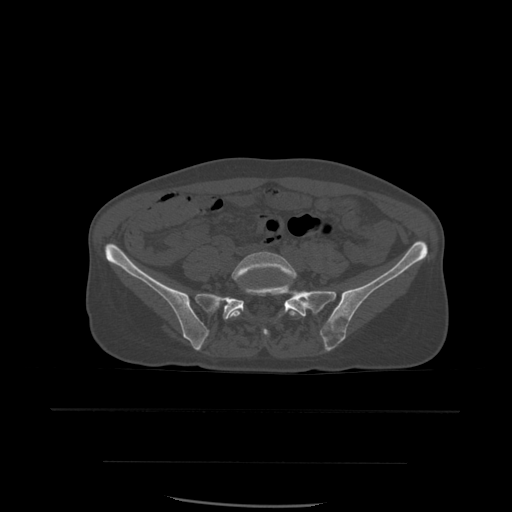
CT including the spine, one axial slice. Position 136 of 574 along the scan axis. Bone window (W 1800 / L 400 HU). 1.25 mm slice thickness. 512 × 512 image matrix, field of view 392 × 392 mm. Patient age 48 years. From the clinical record (not read from this slice): primary cancer: lung; vertebrae with lytic lesions (as recorded): T11.
Outlined on this slice (semi-automatically segmented with operator editing):
- L5 vertebra: box from (x=228, y=252) to (x=304, y=337) px